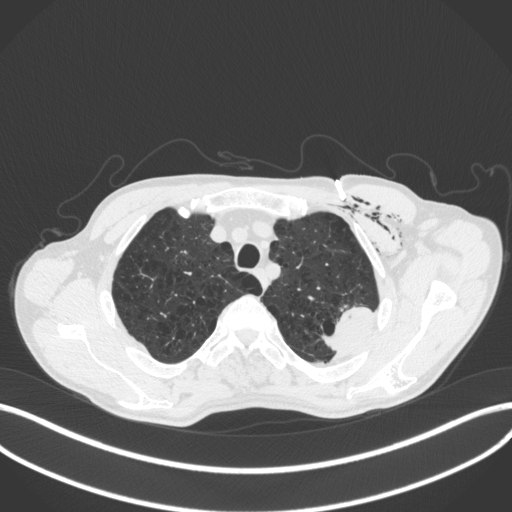
Chest CT, one axial slice. Reconstruction kernel B31f. 120 kVp. Lung window (W 1500 / L -600 HU). 1 mm slice thickness. 512 × 512 image matrix, field of view 400 × 400 mm. Male patient, age 58 years. Case-level facts recorded for this patient, not image findings: clinical TNM (as recorded): T3 N0 M0.
Annotated regions visible in this slice (bounding box drawn by a radiologist):
- lung tumour (recorded histology: adenocarcinoma): bounding box [x1, y1, x2, y2] px = [312, 303, 374, 357]